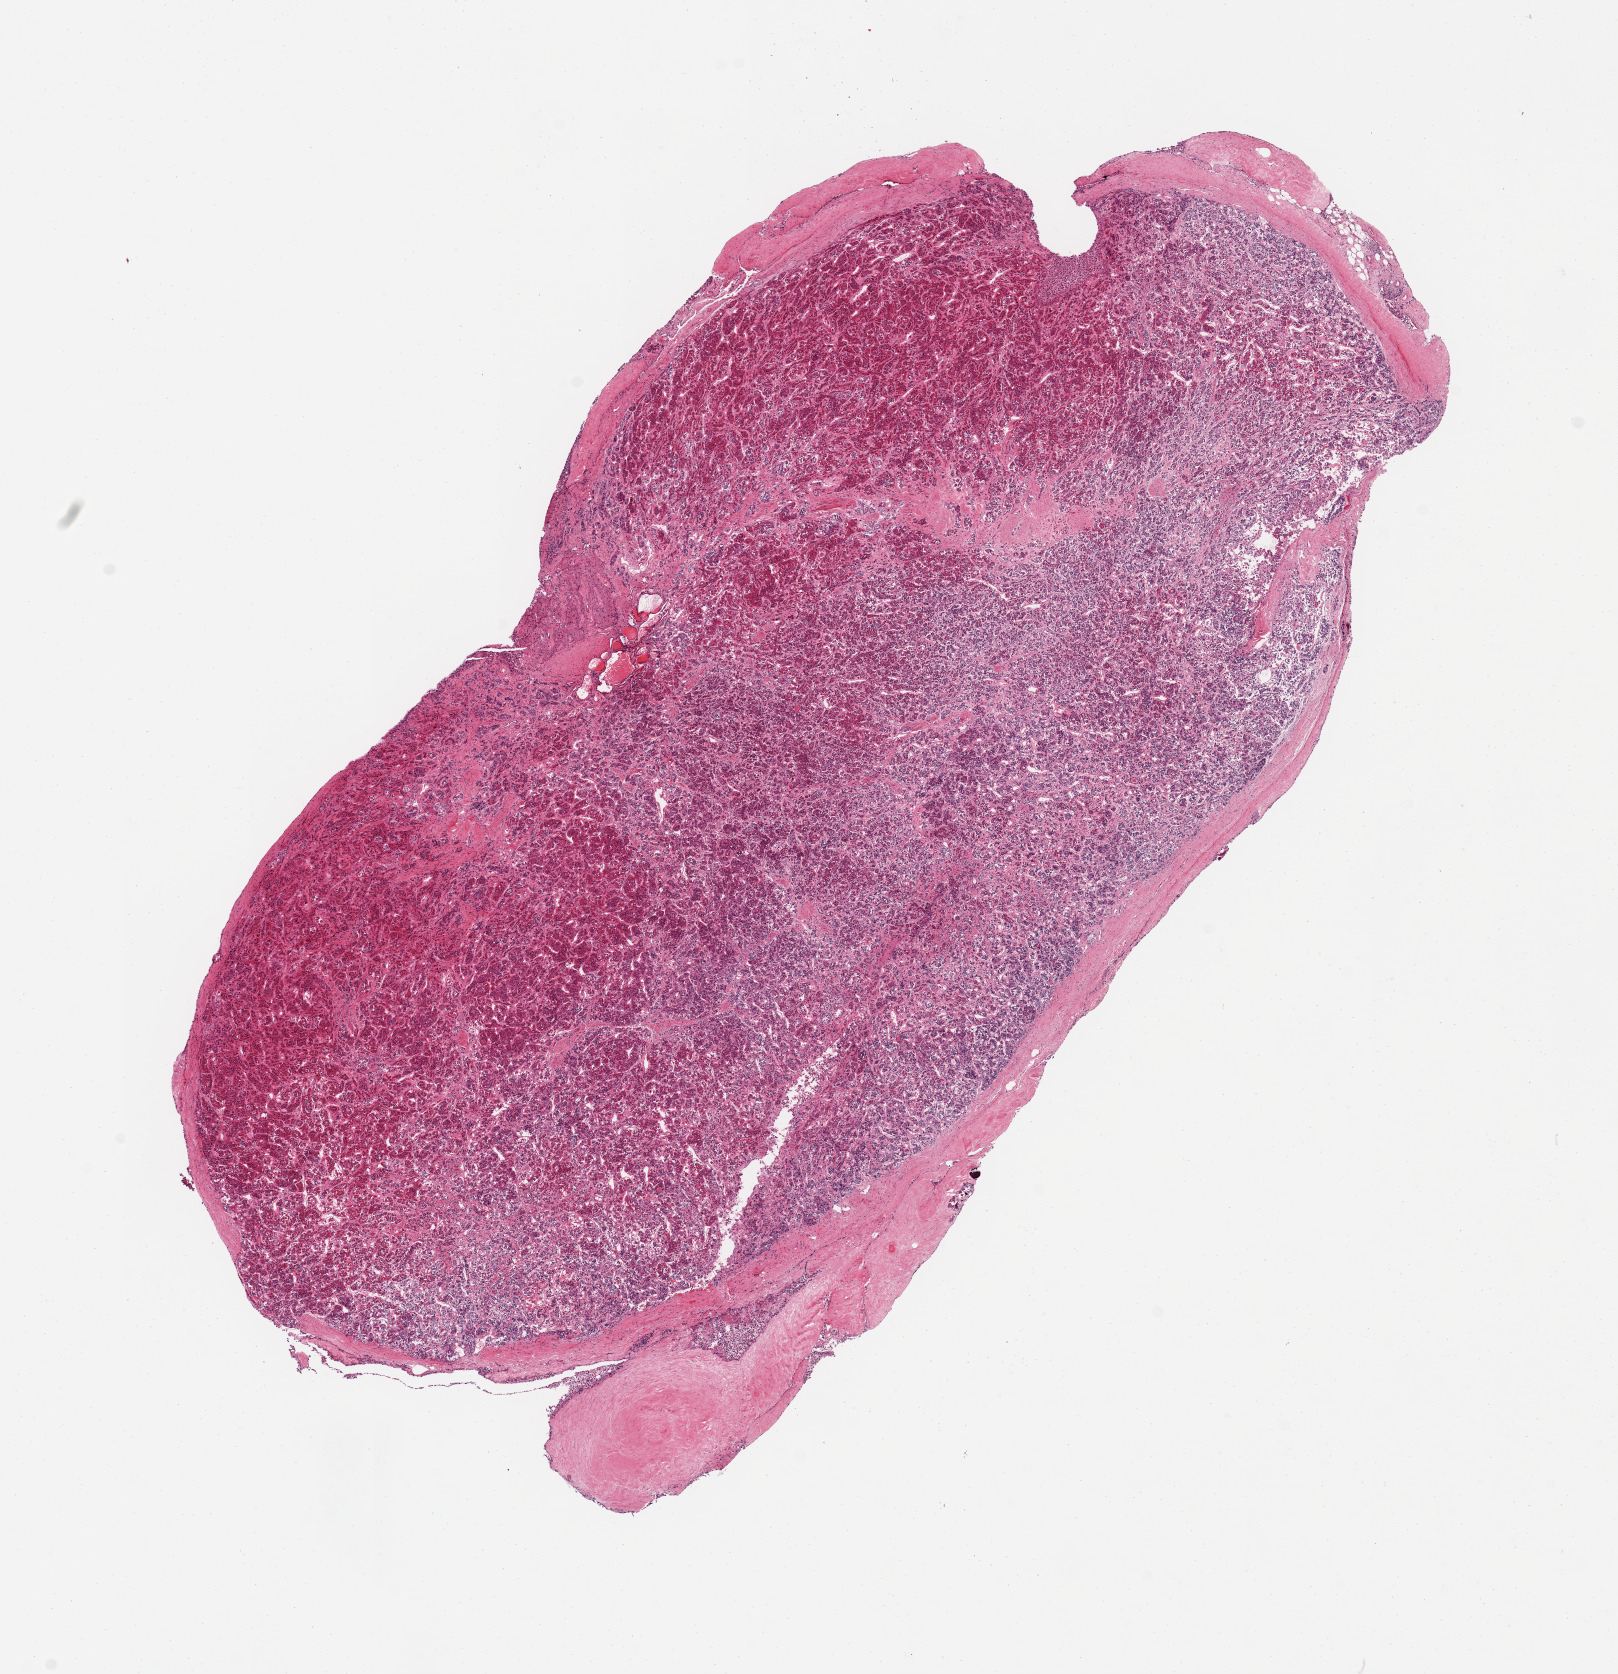
Digitized hematoxylin and eosin (H&E)-stained section — shown as a low-resolution overview of the whole scanned area (about 12.8 x 13.2 mm, slide scanned at 20x). PAXgene-fixed paraffin-embedded (PFPE) section. Target tissue: pituitary. Donor tissue sample. Donor: male.
- pathologist's review note for this sample: 1 piece, adenohypophysis, adherent dura up to ~1mm